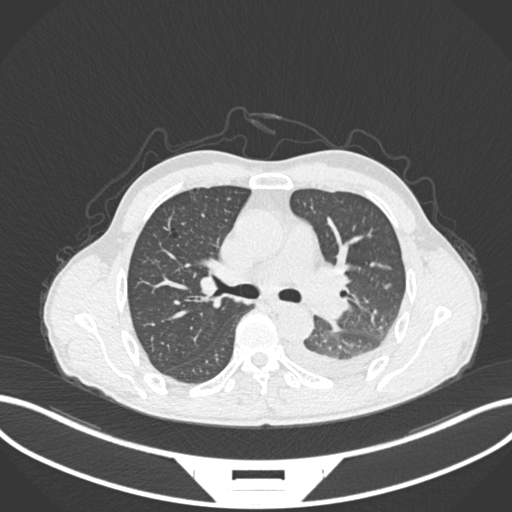
Chest CT, one axial slice; position 157 of 222 along the scan axis; reconstruction kernel B30f; 120 kVp; lung window (W 1500 / L -600 HU); 512 × 512 image matrix, field of view 400 × 400 mm. Male patient, age 47 years. Case-level facts recorded for this patient, not image findings: clinical TNM (as recorded): T3 N1 M1c; histopathological grade: G3.
Structures marked on this image (rectangle marked by the reading radiologist):
- lung tumour (recorded histology: small cell carcinoma): bounding box (x1, y1, x2, y2) in pixels: (313, 296, 348, 322)